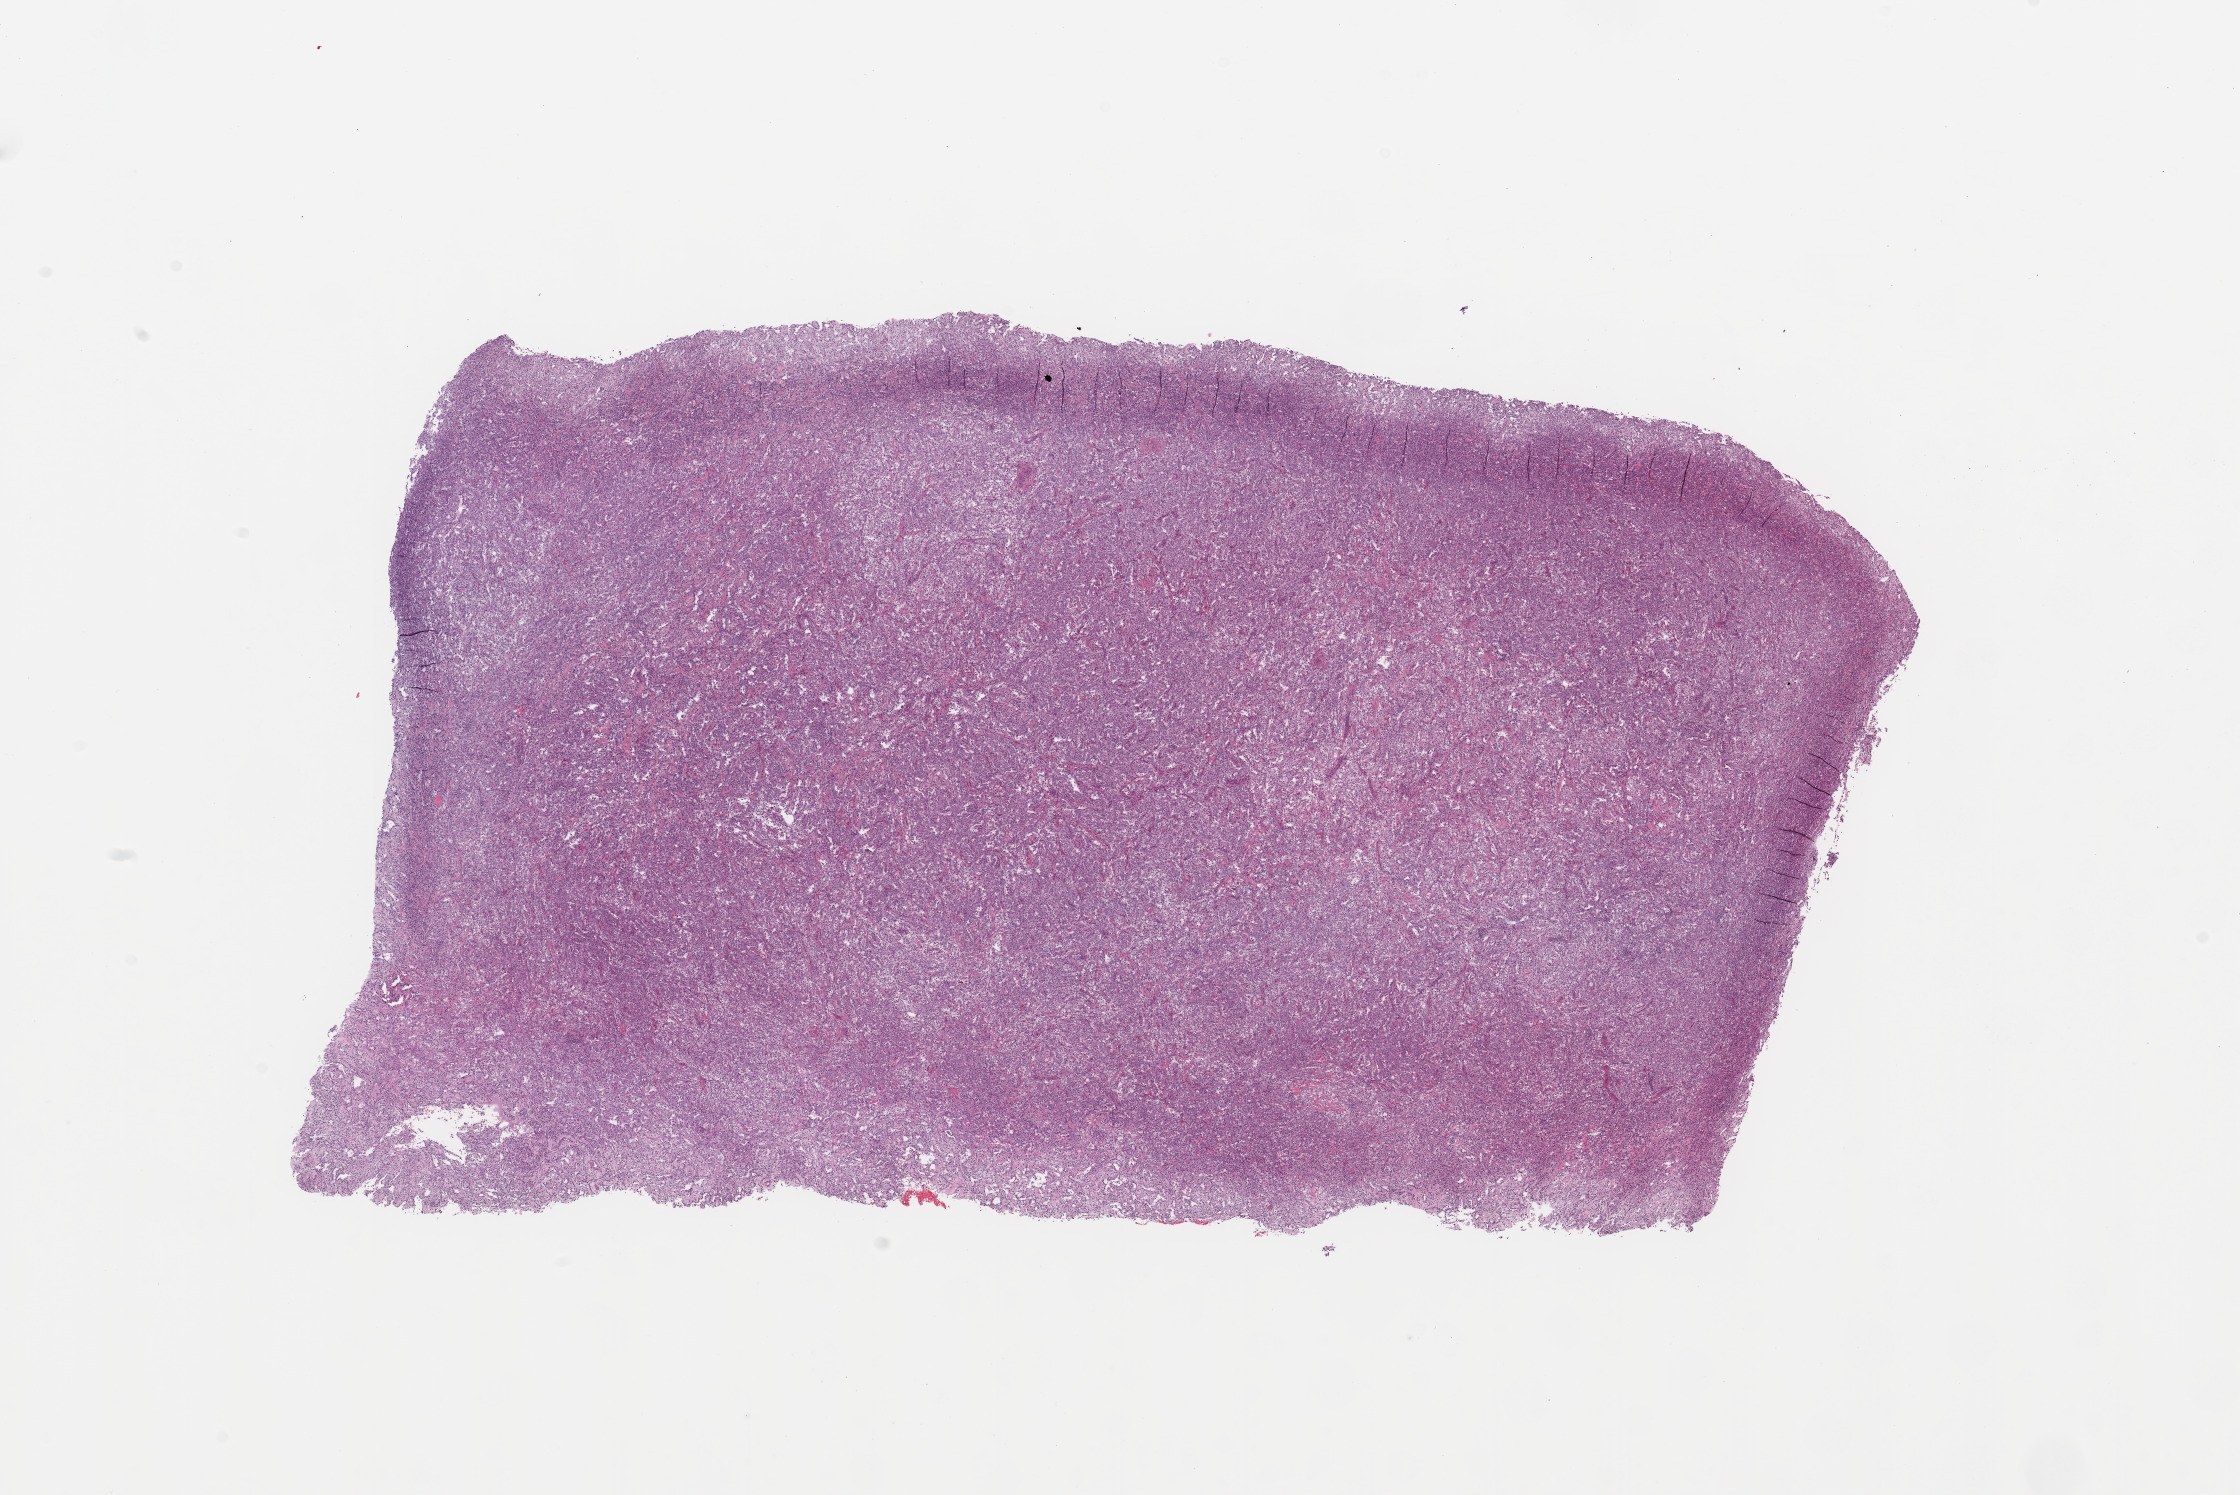
H&E-stained whole-slide image — low-resolution overview of the scanned area, about 17.7 x 11.8 mm (acquisition: 20x scan); tumour tissue sample, kidney. Patient: male, age 61 years. Histologic grade: G4 (undifferentiated).
Diagnosis: Renal cell carcinoma, NOS. AJCC pathologic stage: IV. Primary tumour site (as recorded): upper pole.